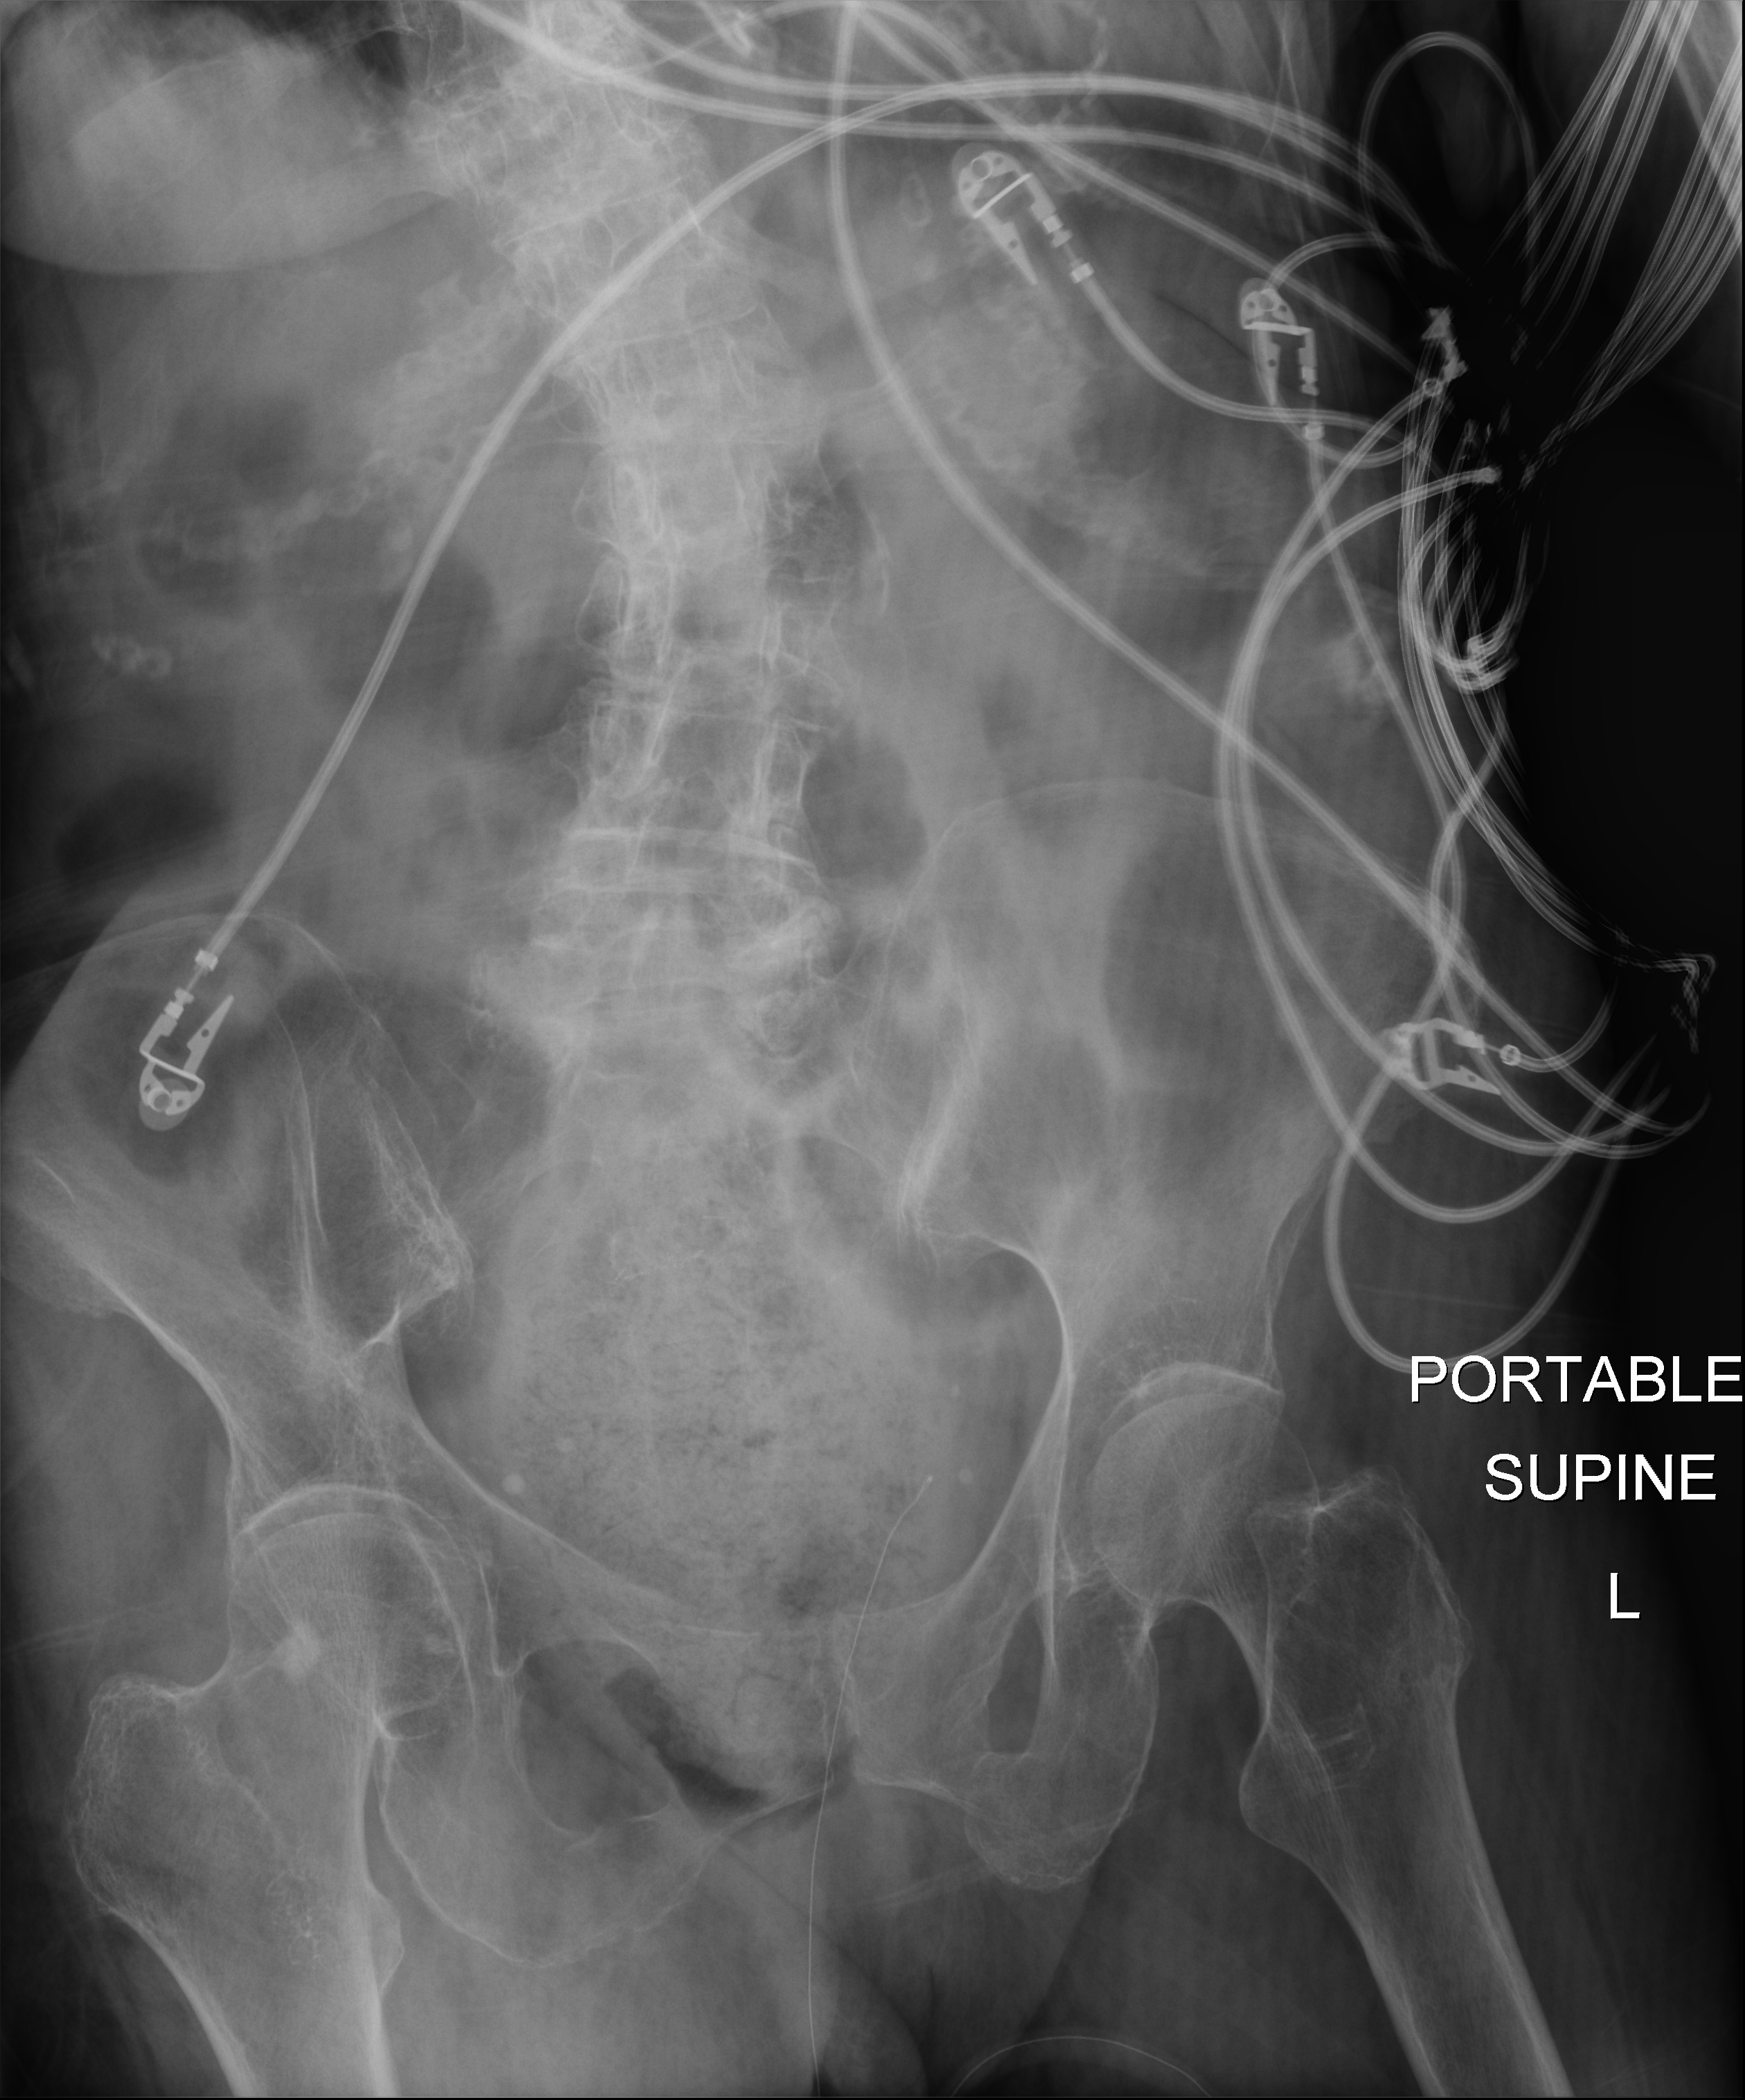
Abdomen X-ray (portable), anteroposterior (AP) projection. Patient hospitalised with COVID-19; female, aged 75–90 years.
Hospital-stay facts (about this admission, not read from this image; timing relative to this image not recorded): diabetes (admission record): no; admitted to intensive care during this hospital stay: no; length of hospital stay: 3 days.